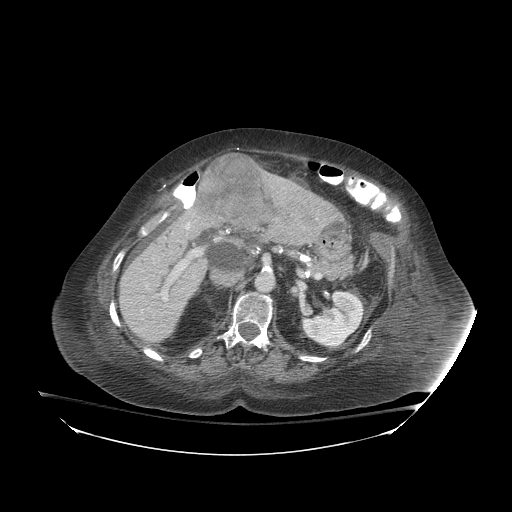
Contrast-enhanced abdominal CT (liver protocol), one axial slice. Position 45 of 81 along the scan axis. Soft-tissue window (W 400 / L 40 HU). 2.5 mm slice thickness. 512 × 512 image matrix. From the clinical record (not read from this slice): diagnosis: hepatocellular carcinoma (patient treated with transarterial chemoembolisation; whether this scan precedes or follows treatment is not stated here); TNM stage (as recorded): Stage-I; Child-Pugh class: B; tumour differentiation: well-moderately differentiated; tumour nodularity: uninodular.
Annotated regions visible in this slice (semi-automatically segmented with operator editing):
- liver parenchyma outside the tumour (the mass and vessels are separate outlines, so this box may not span the whole liver): bounding box (x1, y1, x2, y2) in pixels: (118, 192, 342, 342)
- mass: (199, 154, 277, 227)
- liver vessels: (146, 222, 202, 301)